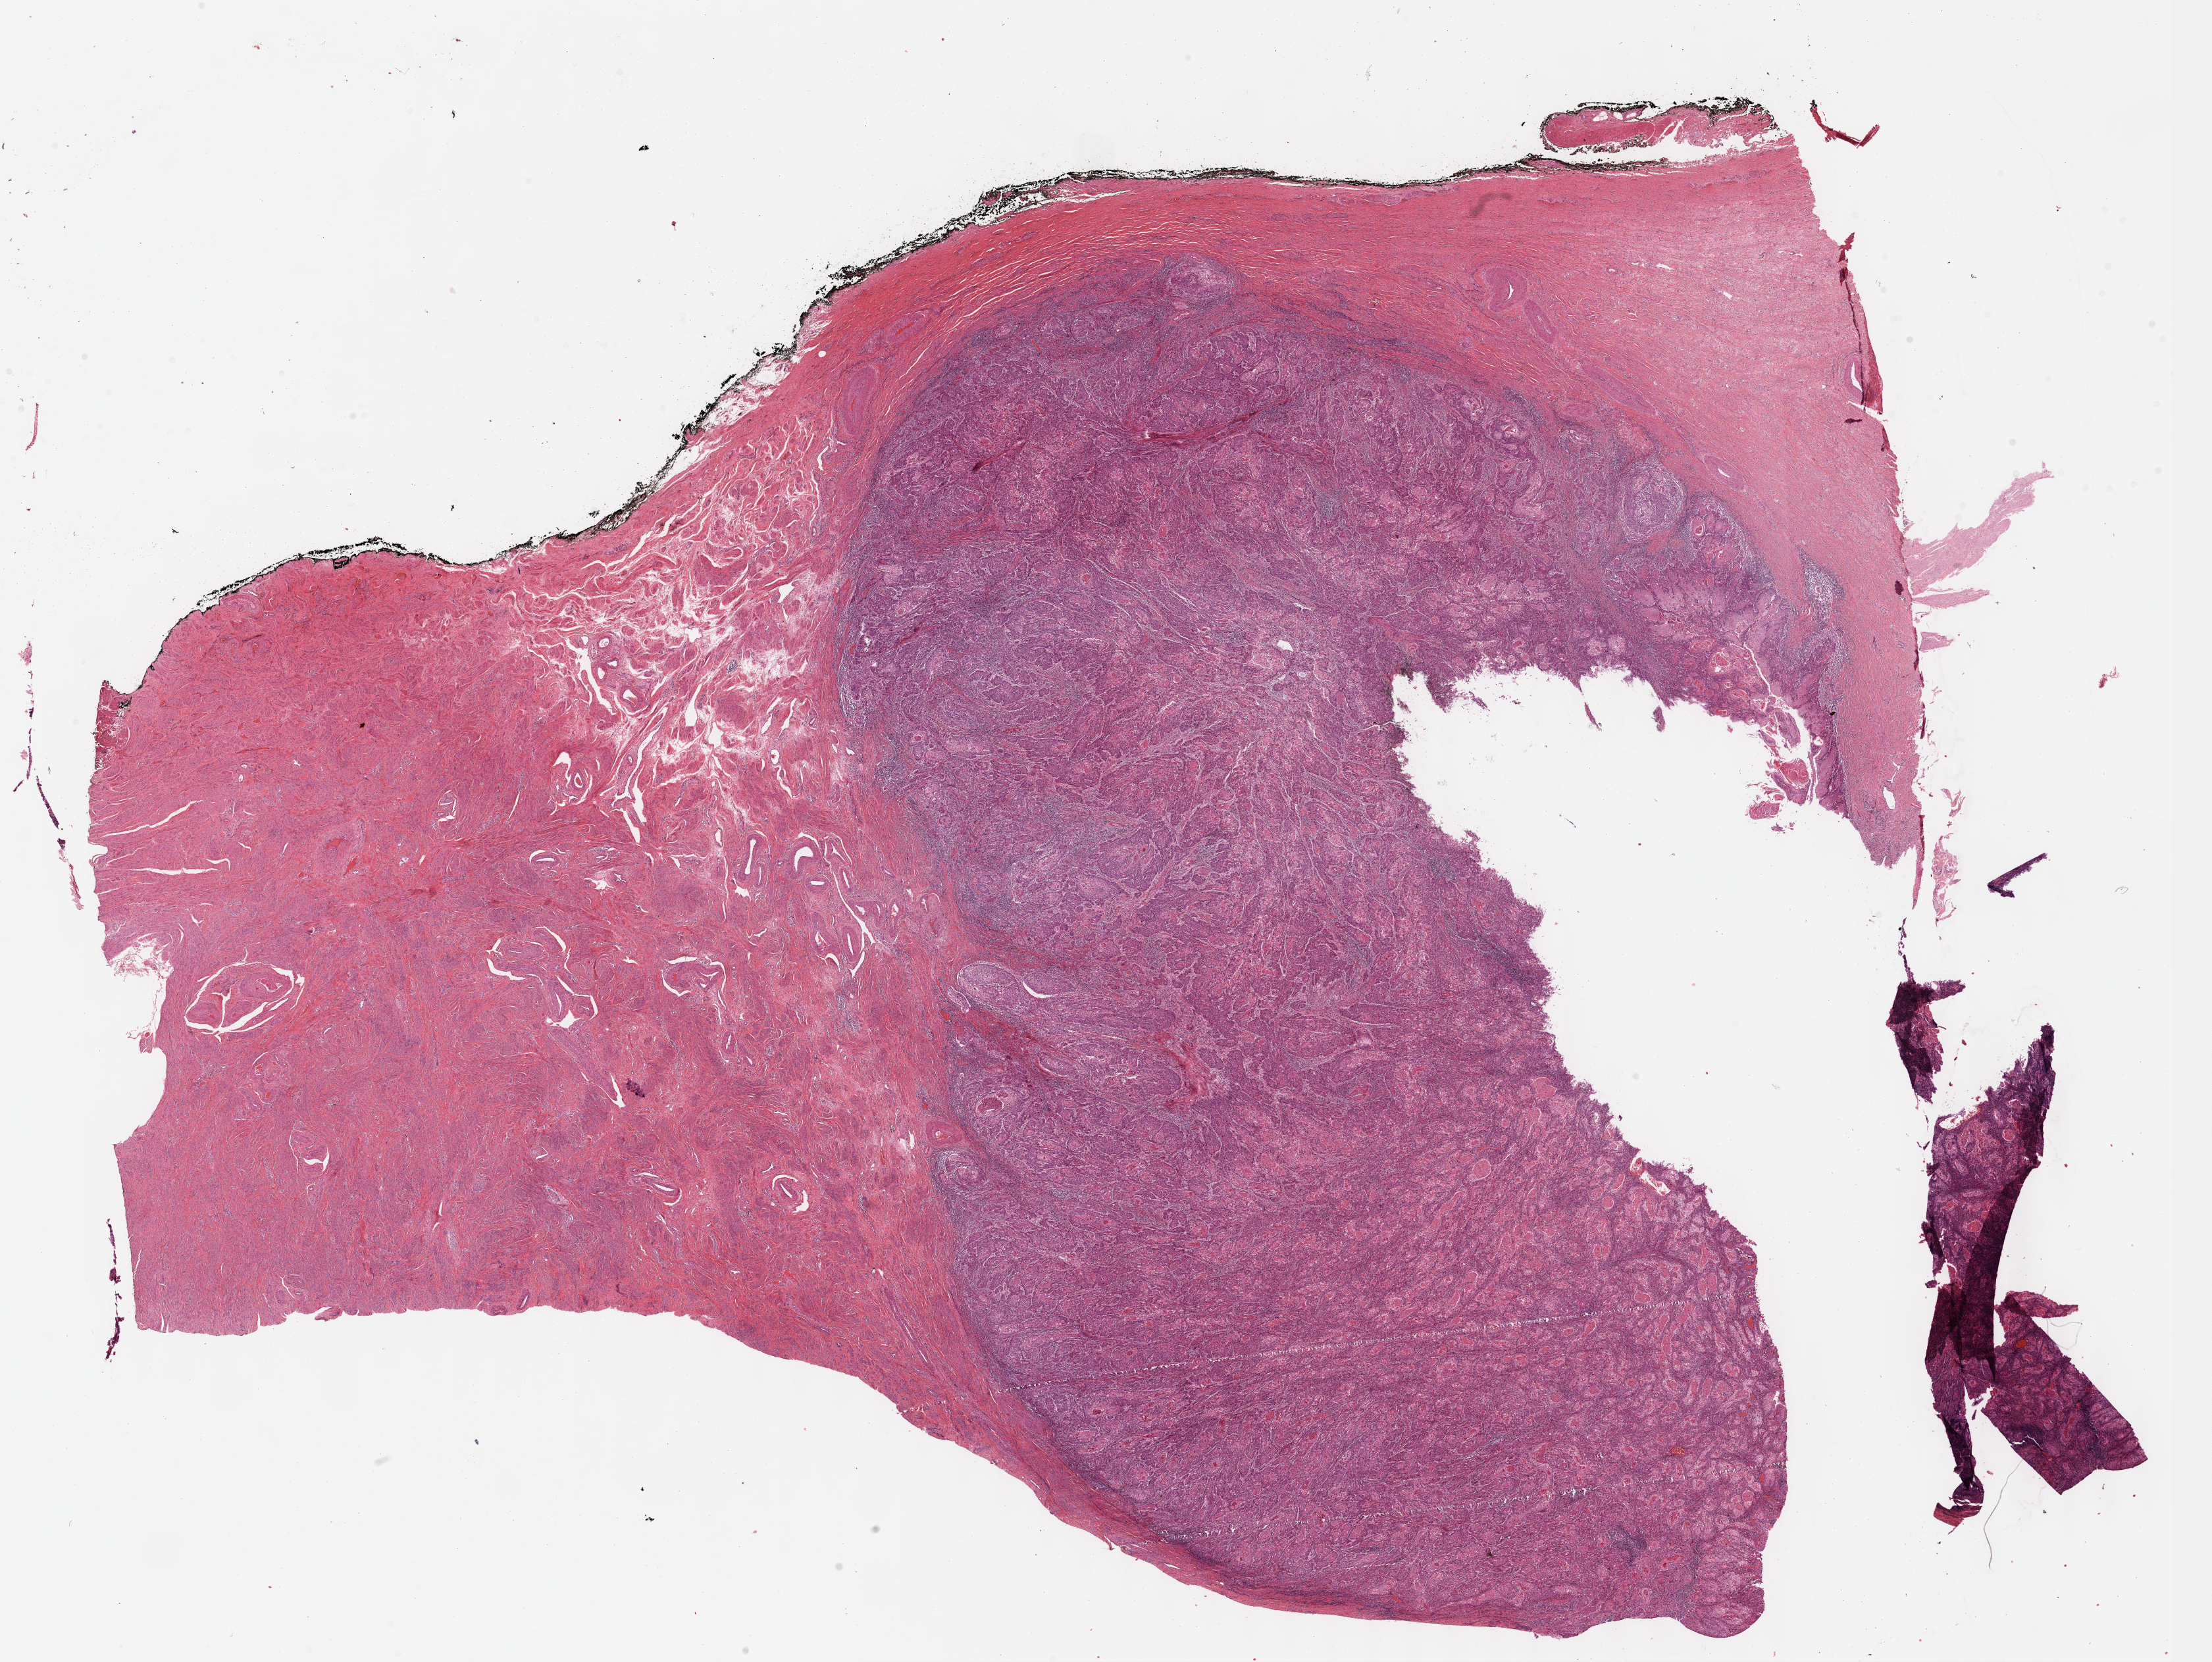
Whole-slide histology image, H&E-stained — whole scanned area (about 27.2 x 20.4 mm) shown as a low-resolution overview, formalin-fixed paraffin-embedded (FFPE) diagnostic section, sample: primary tumour, cervix. Female, age 26 years at initial diagnosis. Histologic grade: G2 (moderately differentiated).
Pathologic diagnosis: Squamous cell carcinoma, NOS (cervix uteri). FIGO stage: IB.